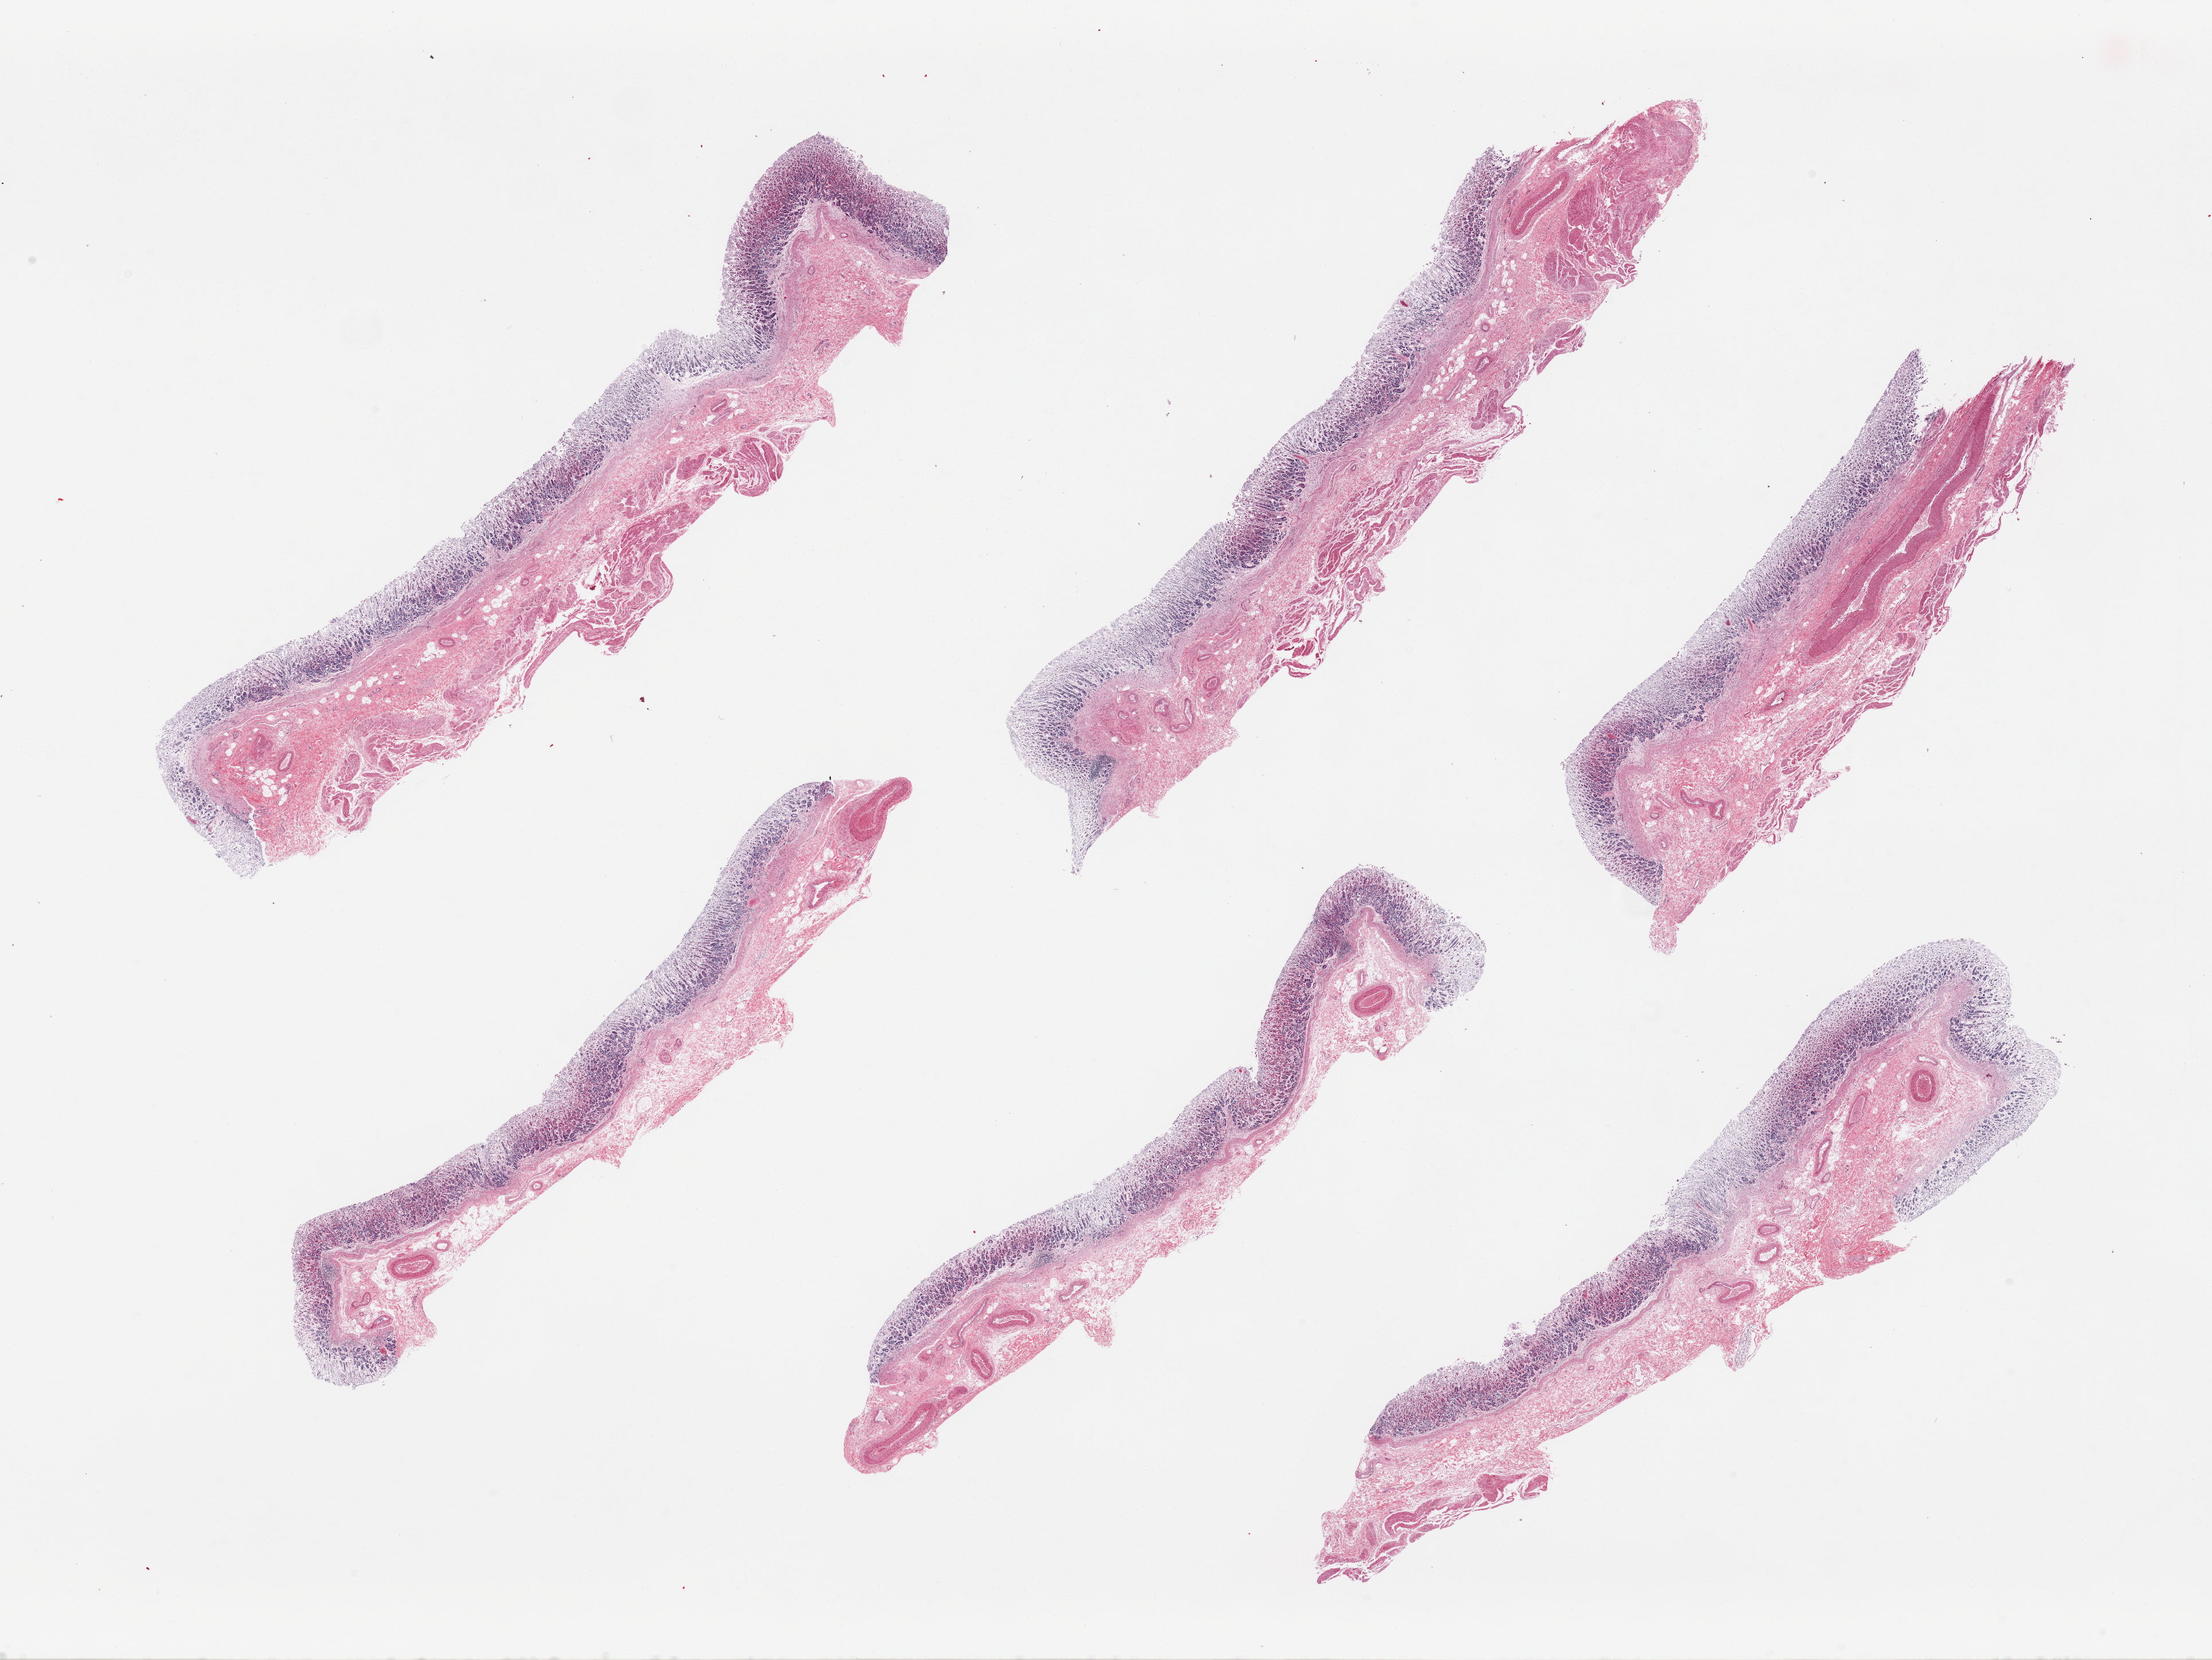
Hematoxylin and eosin (H&E) whole-slide image, brightfield, a low-resolution overview of the entire scanned area, about 30.5 x 22.9 mm; PAXgene-fixed, paraffin-embedded tissue; section of stomach (target tissue); donor tissue sample. Donor: male.
- reviewer comment on this tissue sample: 6 pieces, severely autolyzed mucosa and muscularis